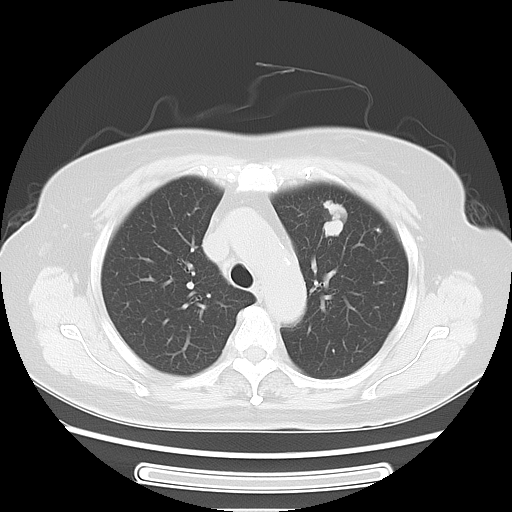
Chest CT, one axial slice; slice 44 of 57 in the series (ordered by position); lung window (W 1500 / L -600 HU); 512 × 512 image matrix, field of view 363 × 363 mm. Patient: female, 77 years. Case-level facts recorded for this patient, not image findings: clinical TNM (as recorded): T1c N3 M0; histopathological grade: G2-3.
Outlined on this slice (rectangle marked by the reading radiologist):
- lung tumour (recorded histology: adenocarcinoma): bounding box (x1, y1, x2, y2) in pixels: (322, 189, 347, 239)